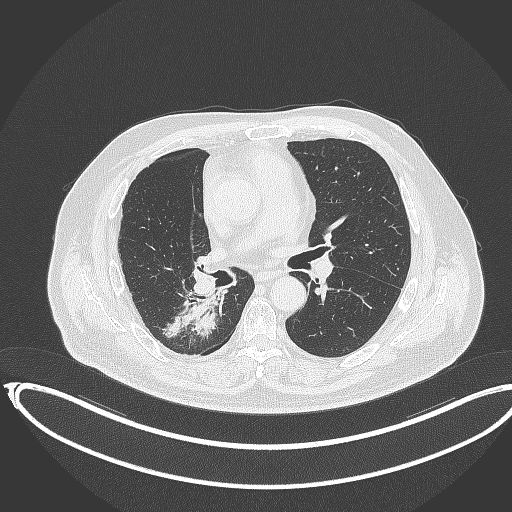
Chest CT, one axial slice. Slice 189 of 403 in the series (ordered by position). Reconstruction kernel B70f. 120 kVp. Lung window (W 1500 / L -600 HU). 512 × 512 image matrix, field of view 436 × 436 mm. Patient: male, 68 years. From the clinical record (not read from this slice): clinical TNM (as recorded): T2a N0 M0.
Outlined on this slice (rectangle marked by the reading radiologist):
- lung tumour (recorded histology: adenocarcinoma): bounding box (x1, y1, x2, y2) in pixels: (164, 290, 235, 345)